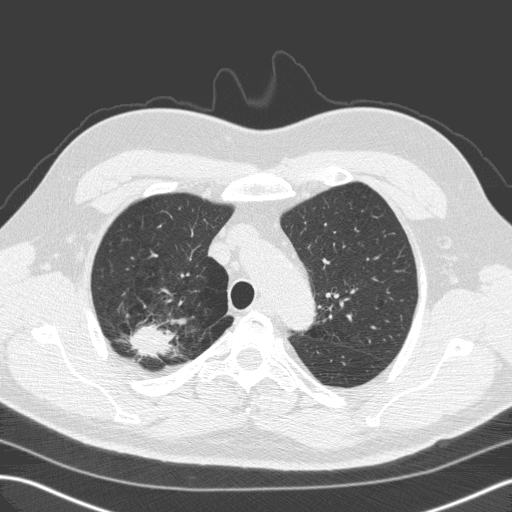
Low-dose screening chest CT, one axial slice; position 120 of 149 along the scan axis; lung window (W 1500 / L -600 HU); 2 mm slice thickness; 512 × 512 image matrix, field of view 357 × 357 mm.
Outlined on this slice (outlined manually by an expert reader):
- lesion 1 (tumor, upper lobe of right lung): bounding box <129,323,174,359> (left, top, right, bottom; pixels)